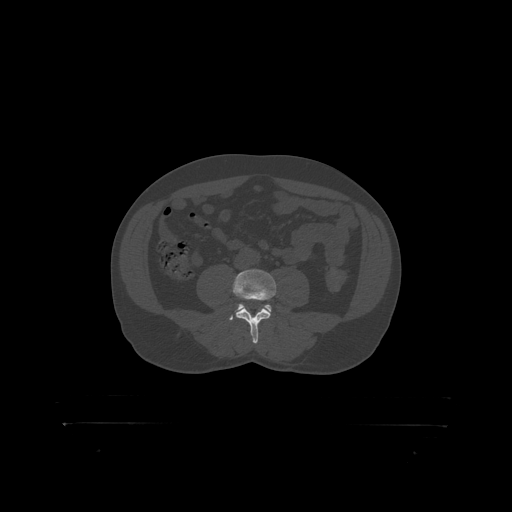
CT including the spine, one axial slice; position 226 of 399 along the scan axis; 120 kVp; bone window (W 1800 / L 400 HU); 1.25 mm slice thickness; 512 × 512 image matrix, field of view 650 × 650 mm. Male patient, age 46 years. From the clinical record (not read from this slice): primary cancer: skin.
Structures marked on this image (semi-automatically segmented with operator editing):
- L4 vertebra: bounding box <233,270,277,319> (left, top, right, bottom; pixels)
- L5 vertebra: <237,304,272,312>